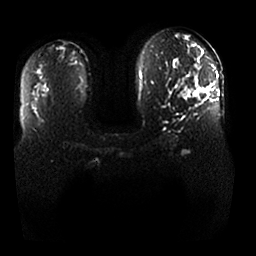
Breast MRI, one axial slice. Slice 17 of 25 in the series (ordered by position). Diffusion-weighted series; image 2 of 4 stored at this slice position (different b-values; order by instance number). 1.5 T. 4 mm slice thickness. 256 × 256 image matrix. Female patient.
Outlined on this slice (expert manual segmentation):
- tumour on diffusion-weighted imaging: bounding box <198,87,209,101> (left, top, right, bottom; pixels)